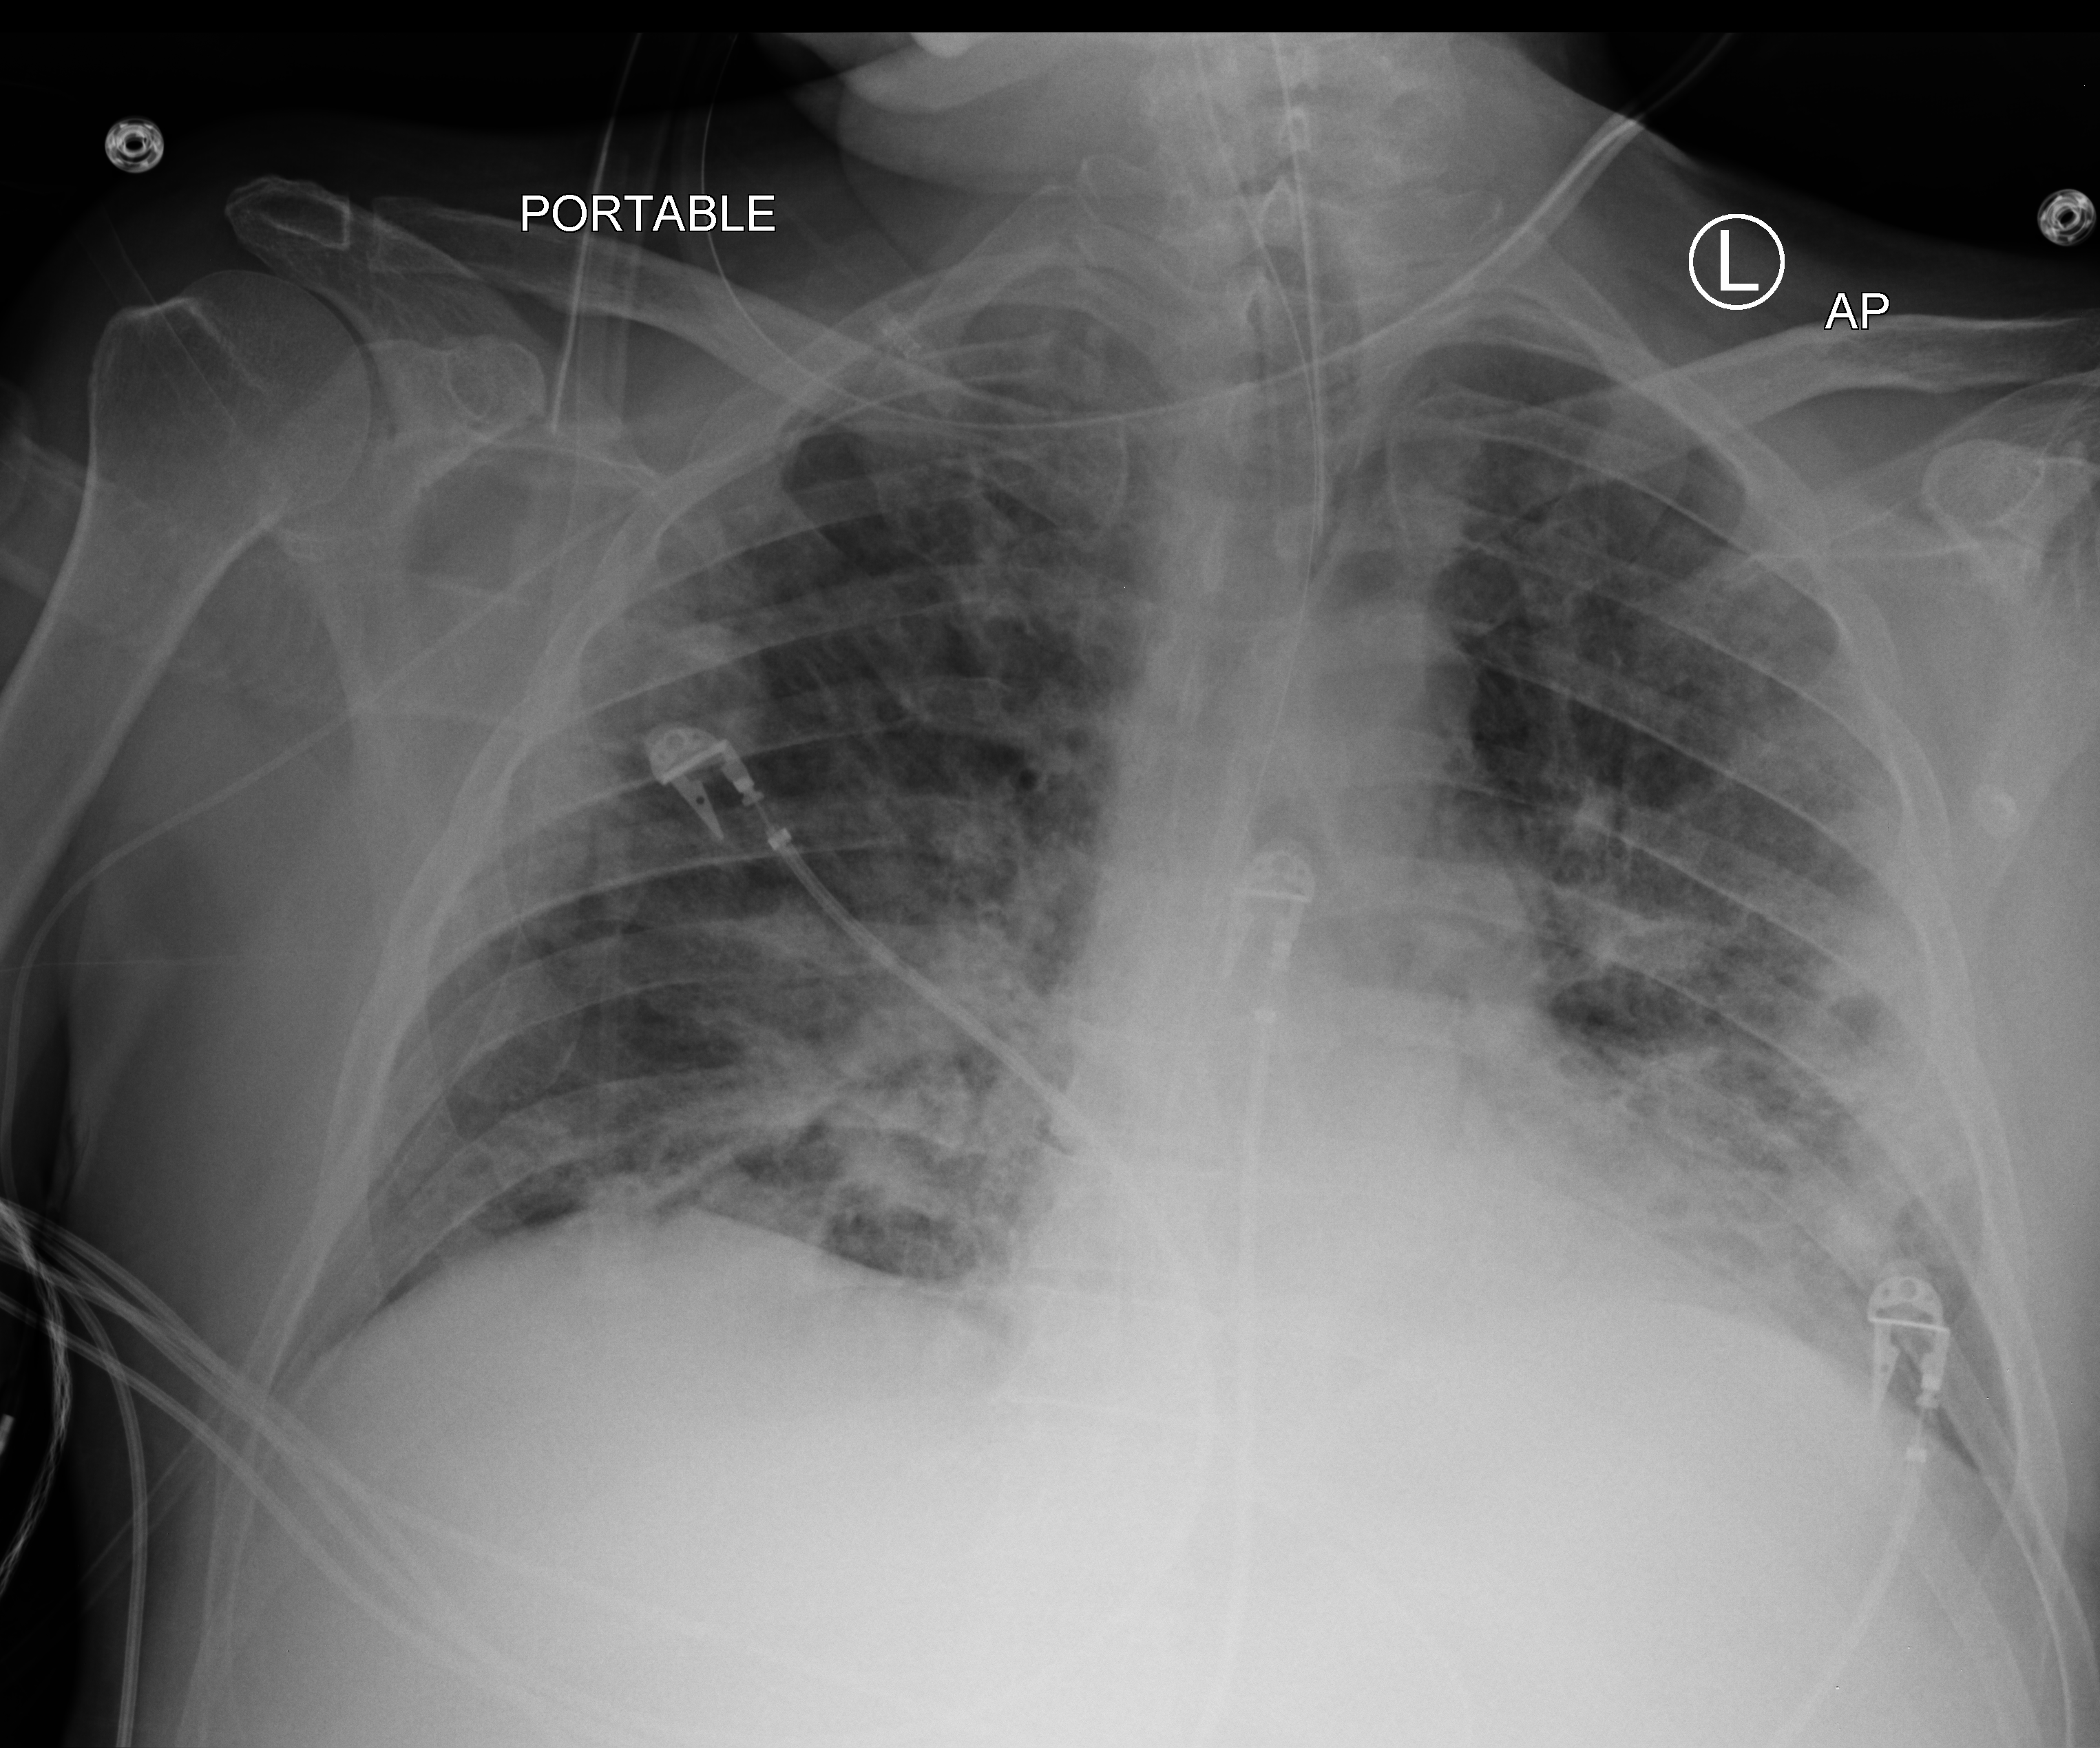
Chest X-ray (portable), anteroposterior (AP) projection. Patient hospitalised with COVID-19; male, aged 60–74 years.
From the hospital-stay record, not from the radiograph (when in the stay this image was taken is not recorded): chronic kidney disease (admission record): no; admitted to intensive care during this hospital stay: yes.